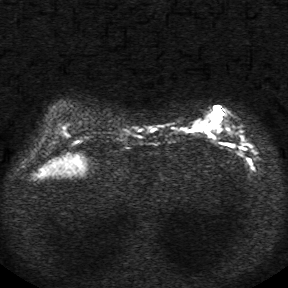
Breast MRI, one axial slice. Position 8 of 34 along the scan axis. Diffusion-weighted series; image 2 of 4 stored at this slice position (different b-values; order by instance number). 1.5 T. 5 mm slice thickness. 288 × 288 image matrix, field of view 340 × 340 mm. Female patient.
Structures marked on this image (expert manual segmentation):
- tumour on diffusion-weighted imaging: bounding box [x1, y1, x2, y2] px = [193, 107, 221, 130]